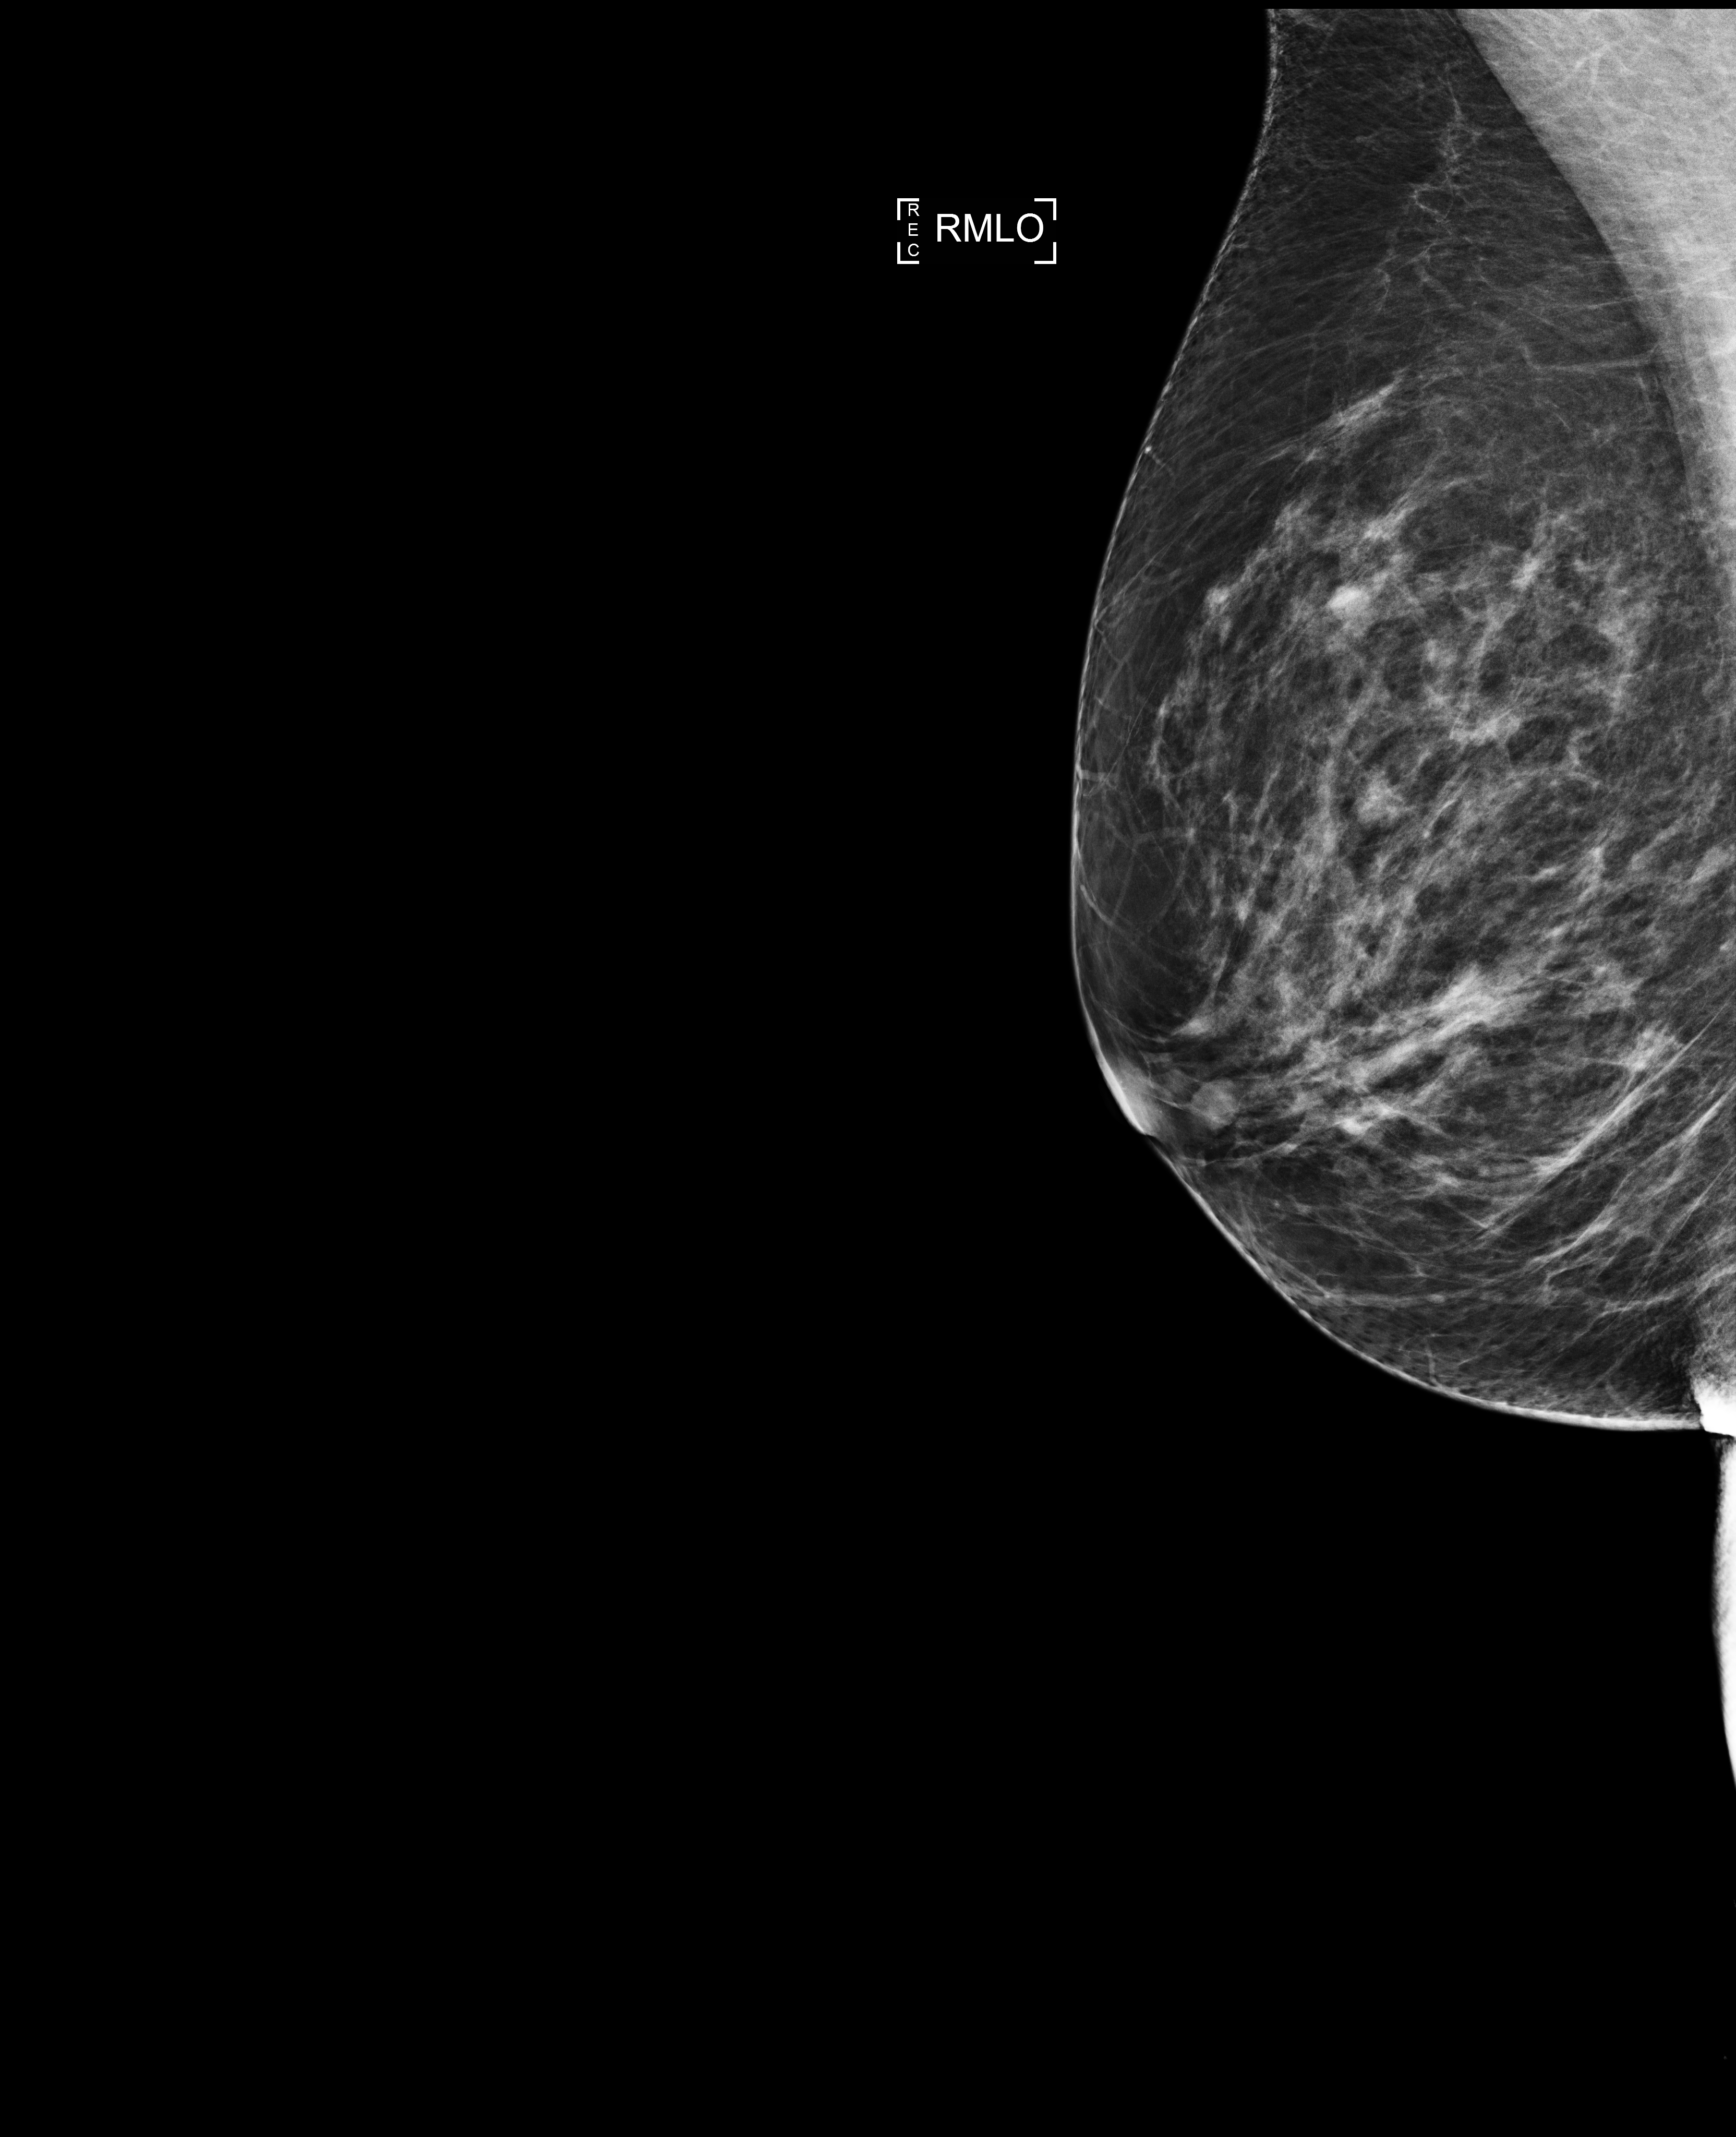
Screening examination, compressed breast thickness 75 mm. Patient aged 53 years (female).
Image type: full-field digital mammogram. Breast: right. Projection: mediolateral oblique (MLO) view.